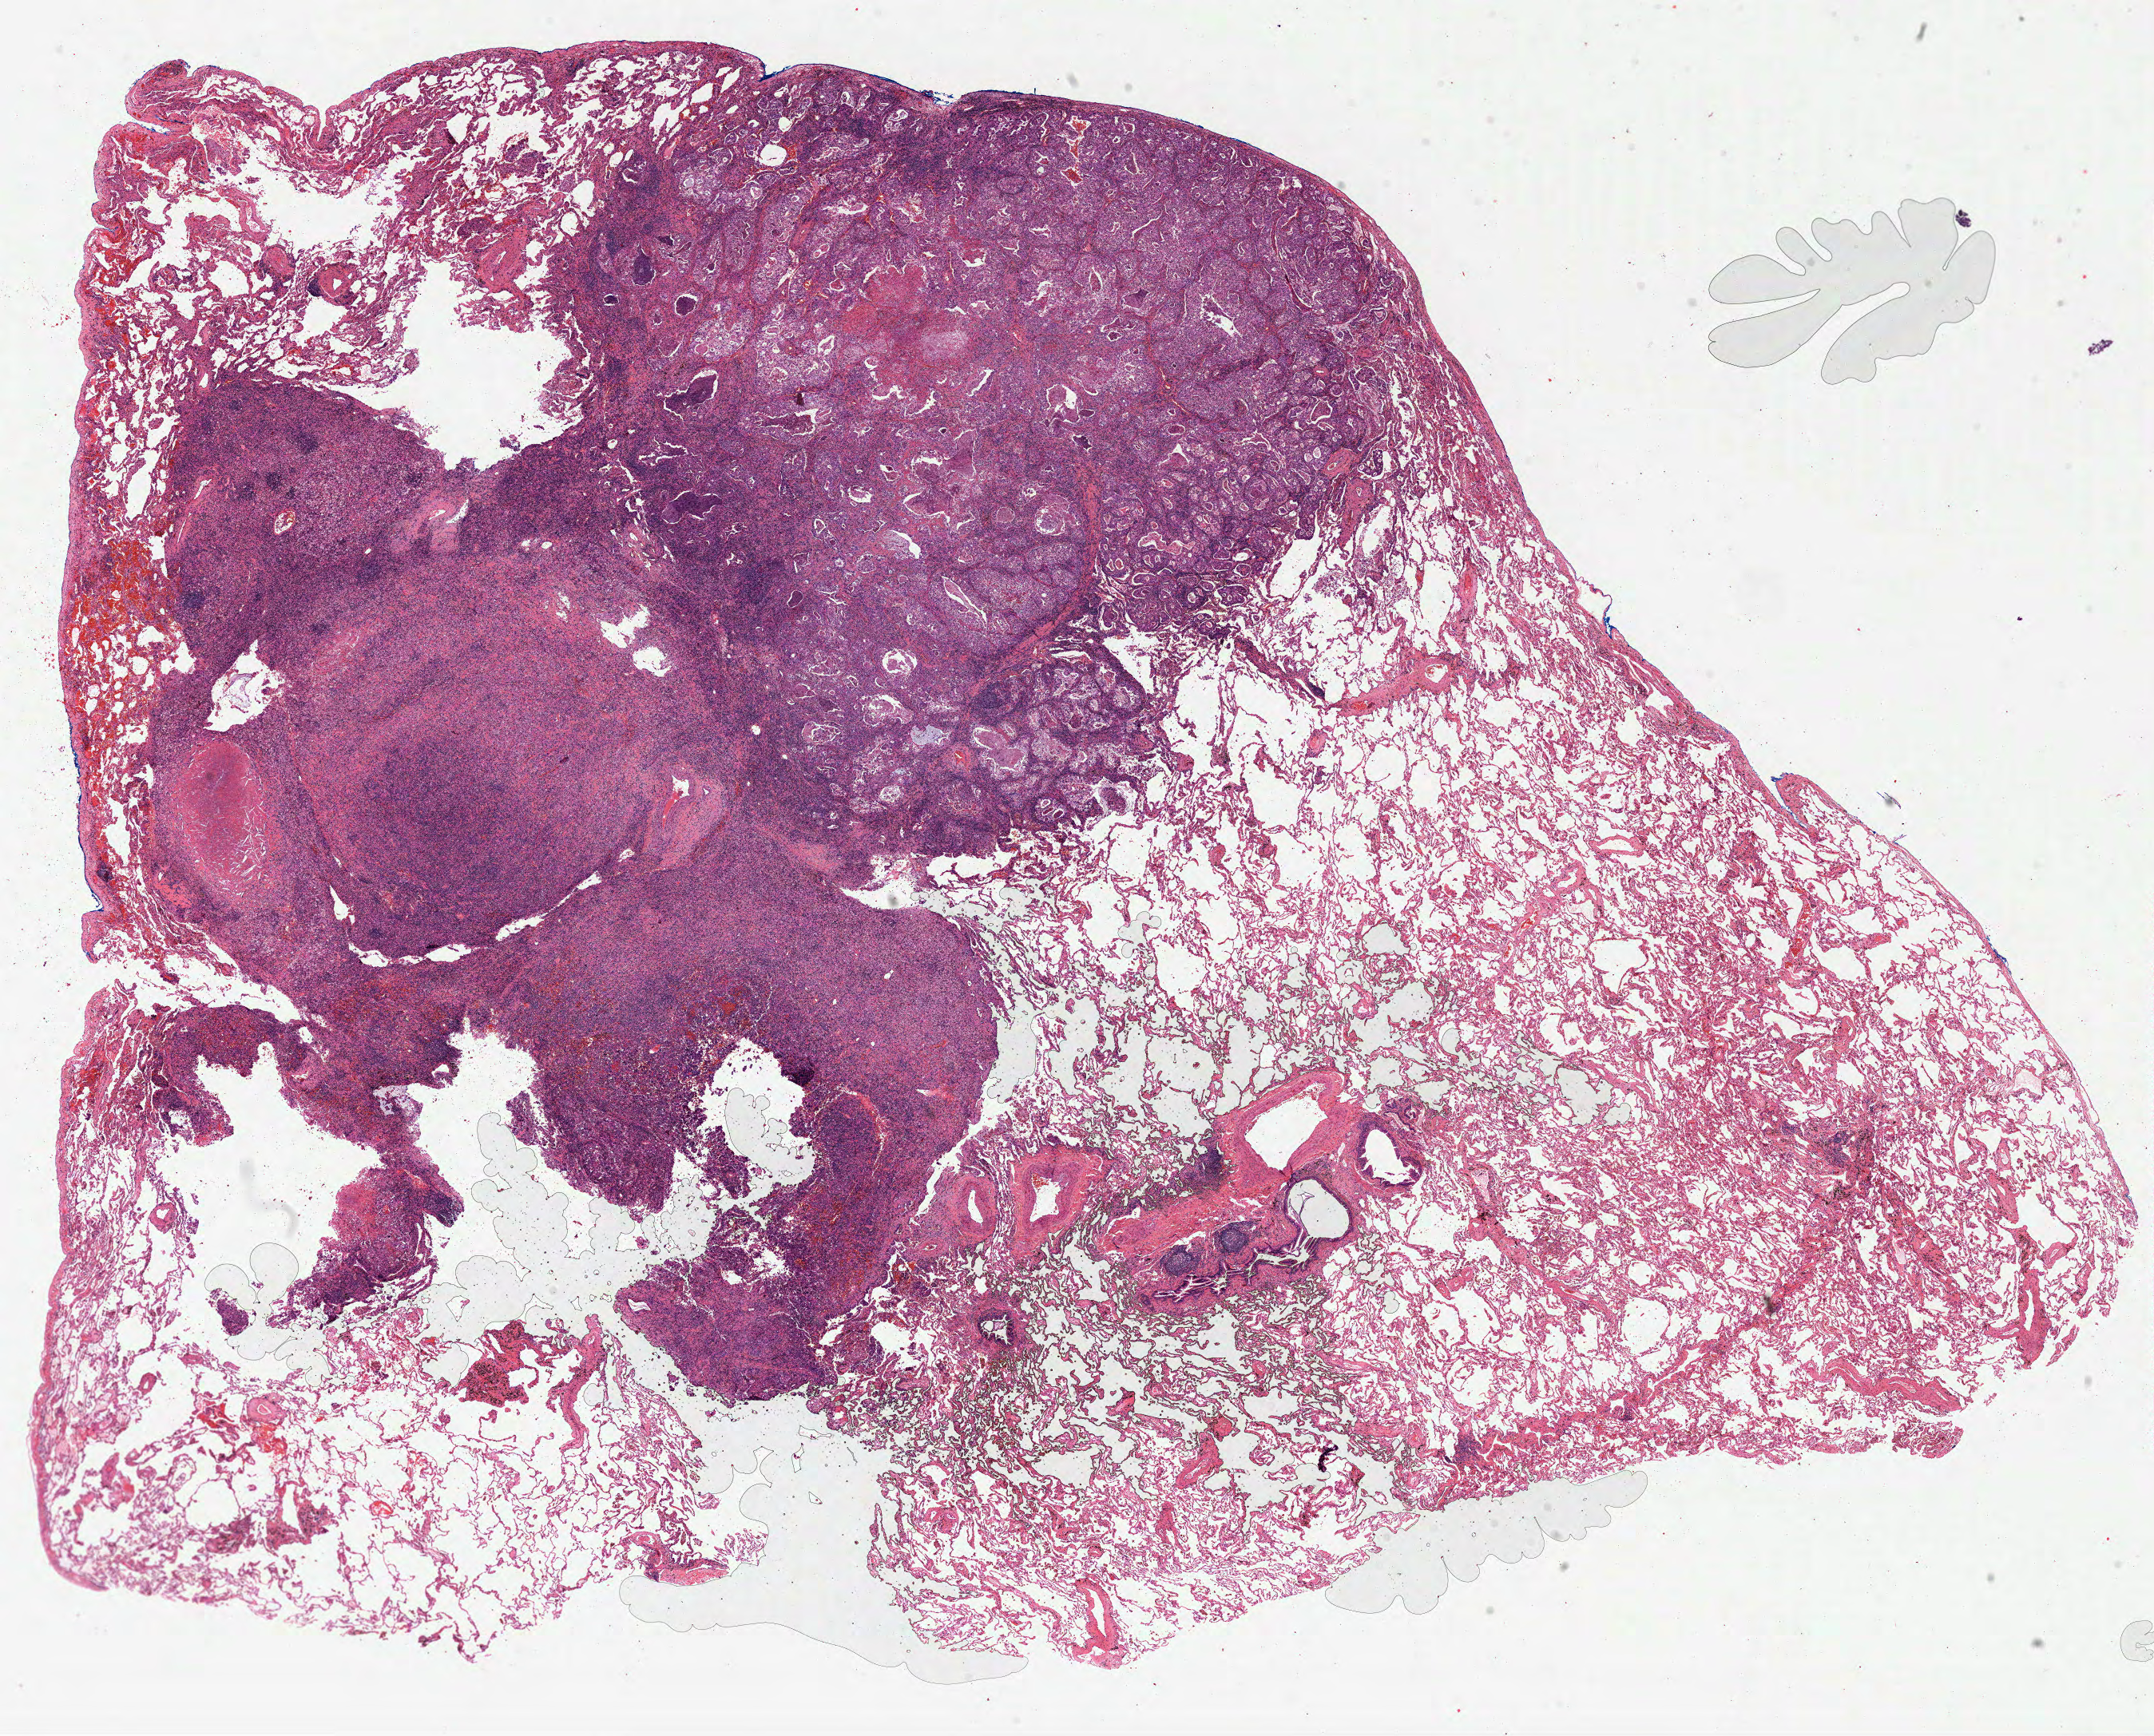
Whole-slide histology image, H&E-stained, whole scanned area (about 21.8 x 17.5 mm) shown as a low-resolution overview, formalin-fixed paraffin-embedded (FFPE) diagnostic section, sample: primary tumour, lung. Patient: male, age at initial diagnosis 71 years.
• histologic diagnosis: Solid carcinoma, NOS
• AJCC pathologic stage: IA (7th edition)
• laterality: right